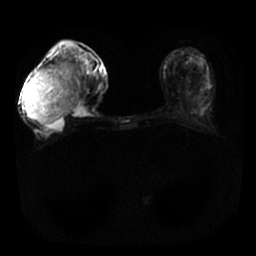
Breast MRI, one axial slice. Slice 4 of 25 in the series (ordered by position). Diffusion-weighted series; image 2 of 4 stored at this slice position (different b-values; order by instance number). 1.5 T. 256 × 256 image matrix, field of view 340 × 340 mm. Female patient.
Structures marked on this image (outlined manually by an expert reader):
- tumour on diffusion-weighted imaging: bounding box (x1, y1, x2, y2) in pixels: (27, 60, 80, 124)